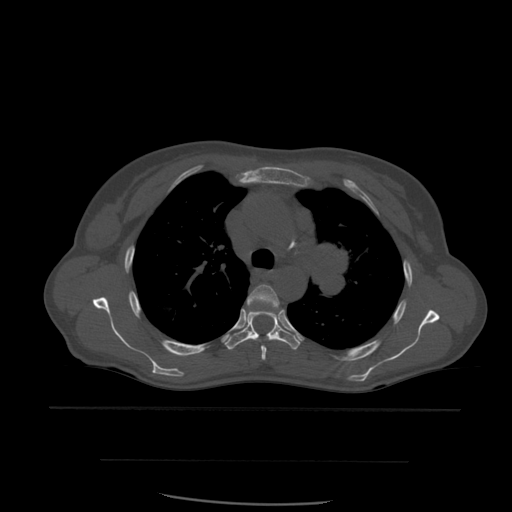
CT including the spine, one axial slice; slice 416 of 574 in the series (ordered by position); bone window (W 1800 / L 400 HU); 512 × 512 image matrix. Patient age 48 years. Case-level facts recorded for this patient, not image findings: primary cancer: lung; vertebrae with lytic lesions (as recorded): T11.
Structures marked on this image (semi-automatic segmentation, software-assisted and operator-edited):
- T4 vertebra: bounding box [x1, y1, x2, y2] px = [247, 285, 280, 361]
- T5 vertebra: [225, 309, 301, 350]